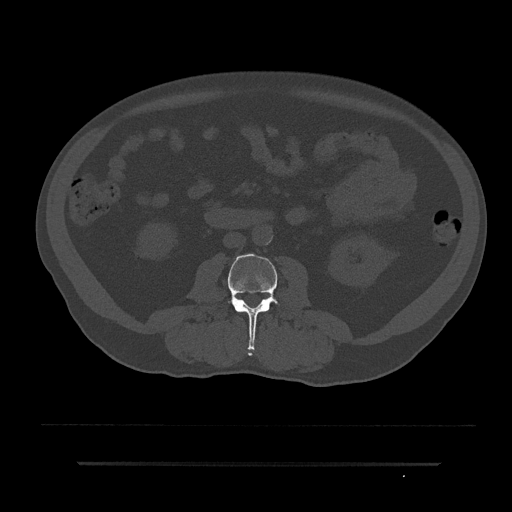
CT including the spine, one axial slice; reconstruction kernel Br40s/3; bone window (W 1800 / L 400 HU); 0.5 mm slice thickness; 512 × 512 image matrix. Patient: male, 59 years. From the clinical record (not read from this slice): primary cancer: bile ducts; vertebrae with lytic lesions (as recorded): T10.
Structures marked on this image (semi-automatic segmentation, software-assisted and operator-edited):
- L3 vertebra: bounding box <222,254,288,350> (left, top, right, bottom; pixels)